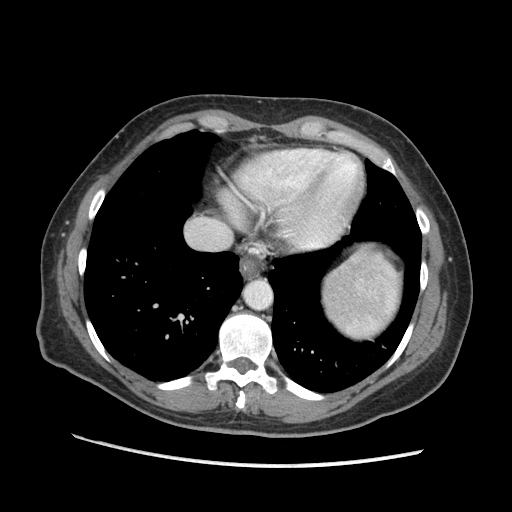
Contrast-enhanced abdominal CT (liver protocol), one axial slice; slice 158 of 170 in the series (ordered by position); reconstruction kernel STANDARD; soft-tissue window (W 400 / L 40 HU); 512 × 512 image matrix, field of view 360 × 360 mm. From the clinical record (not read from this slice): diagnosis: hepatocellular carcinoma (patient treated with transarterial chemoembolisation; whether this scan precedes or follows treatment is not stated here); TNM stage (as recorded): Stage-II; Child-Pugh class: A; tumour differentiation: no biopsy; tumour nodularity: multinodular.
Outlined on this slice (semi-automatically segmented with operator editing):
- abdominal aorta: bounding box (x1, y1, x2, y2) in pixels: (246, 282, 270, 308)